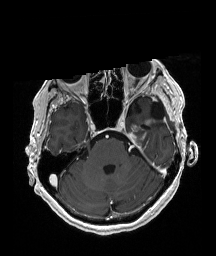
Brain MRI from a brain-tumour surgery series, one axial slice; position 135 of 192 along the scan axis; T1-weighted post-contrast; 216 × 256 image matrix, field of view 211 × 250 mm. Case-level facts recorded for this patient, not image findings: histopathology: Glioblastoma; WHO grade: 4; IDH mutation: no; tumour location: Left Temporal.
Outlined on this slice (outlined manually by an expert reader):
- previous resection cavity: box from (x=151, y=102) to (x=163, y=119) px